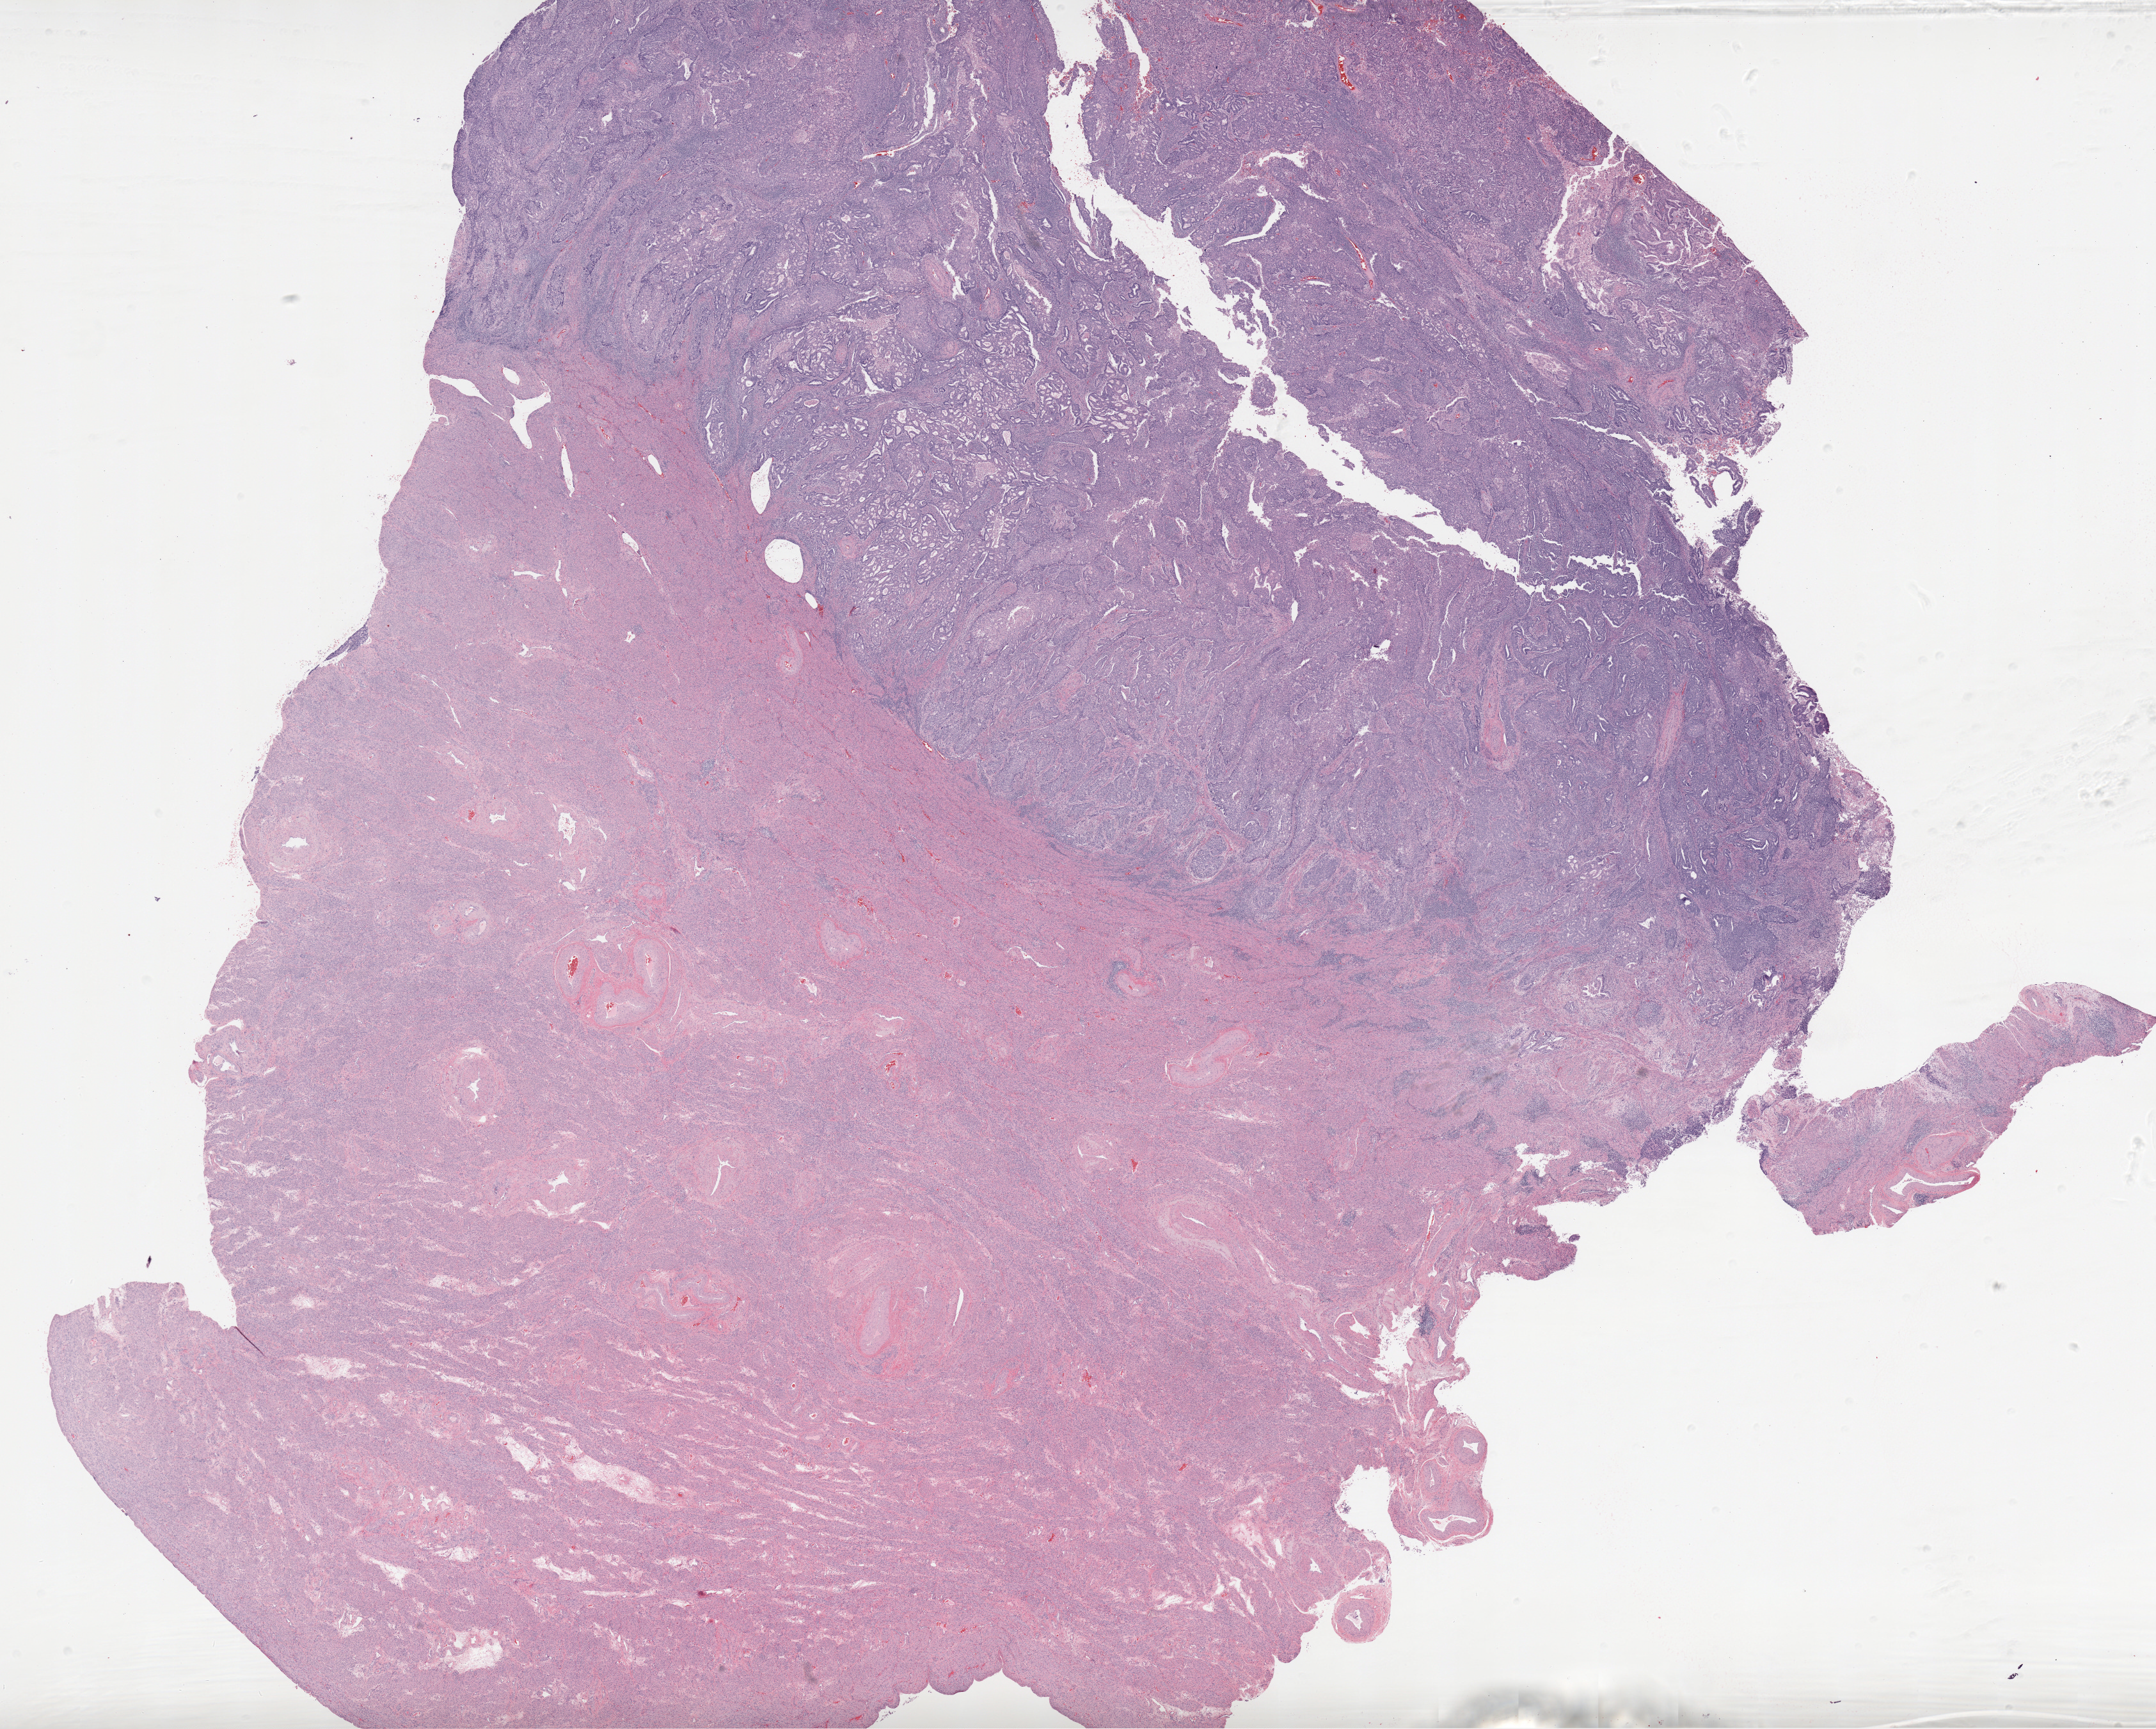
Digitized Hematoxylin and eosin (H&E) stained tissue section (whole slide), a low-resolution overview of the entire scanned area, about 26.9 x 21.5 mm (acquisition: 20x scan), formalin-fixed paraffin-embedded (FFPE) diagnostic section, uterus, primary tumour sample. Female patient; age at initial diagnosis 53 years. Histologic grade: G3 (poorly differentiated).
* FIGO stage: IA
* lymph nodes positive (case pathology): 0 of 7 examined
* histologic diagnosis: Endometrioid adenocarcinoma, NOS (endometrium)